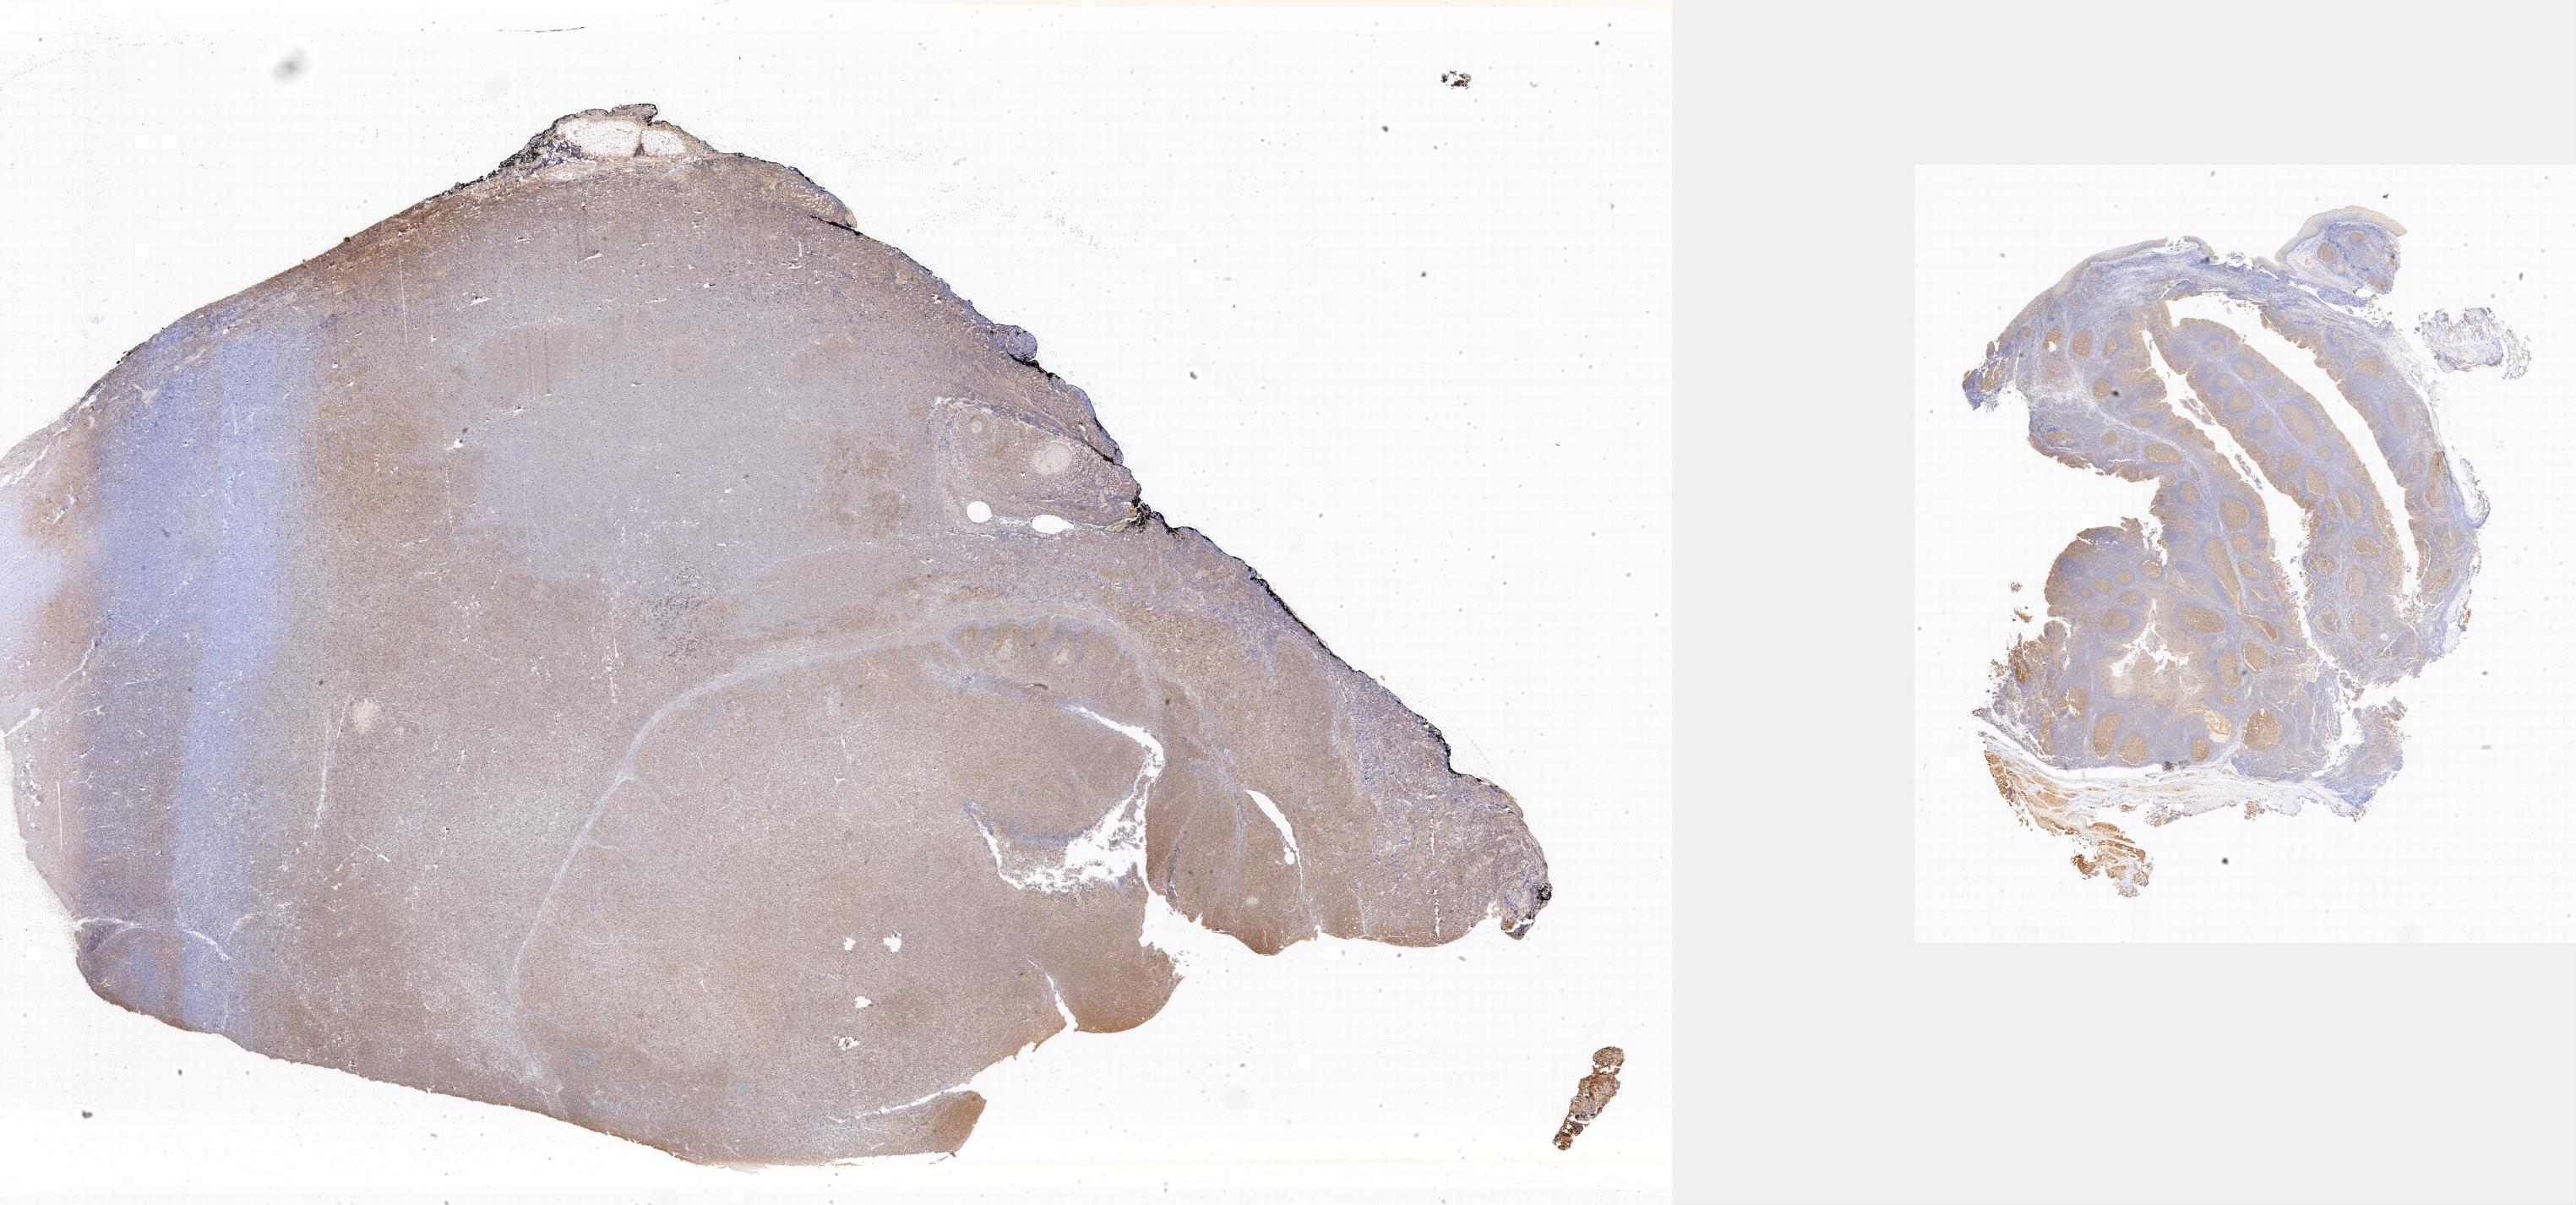
Whole-slide image, immunohistochemical stain for BCL6, a low-resolution overview of the entire scanned area, specimen: tumor tissue, anatomic site: lymph node of head and neck. Male, age 6 years at initial diagnosis.
* diagnosis: Burkitt lymphoma, NOS